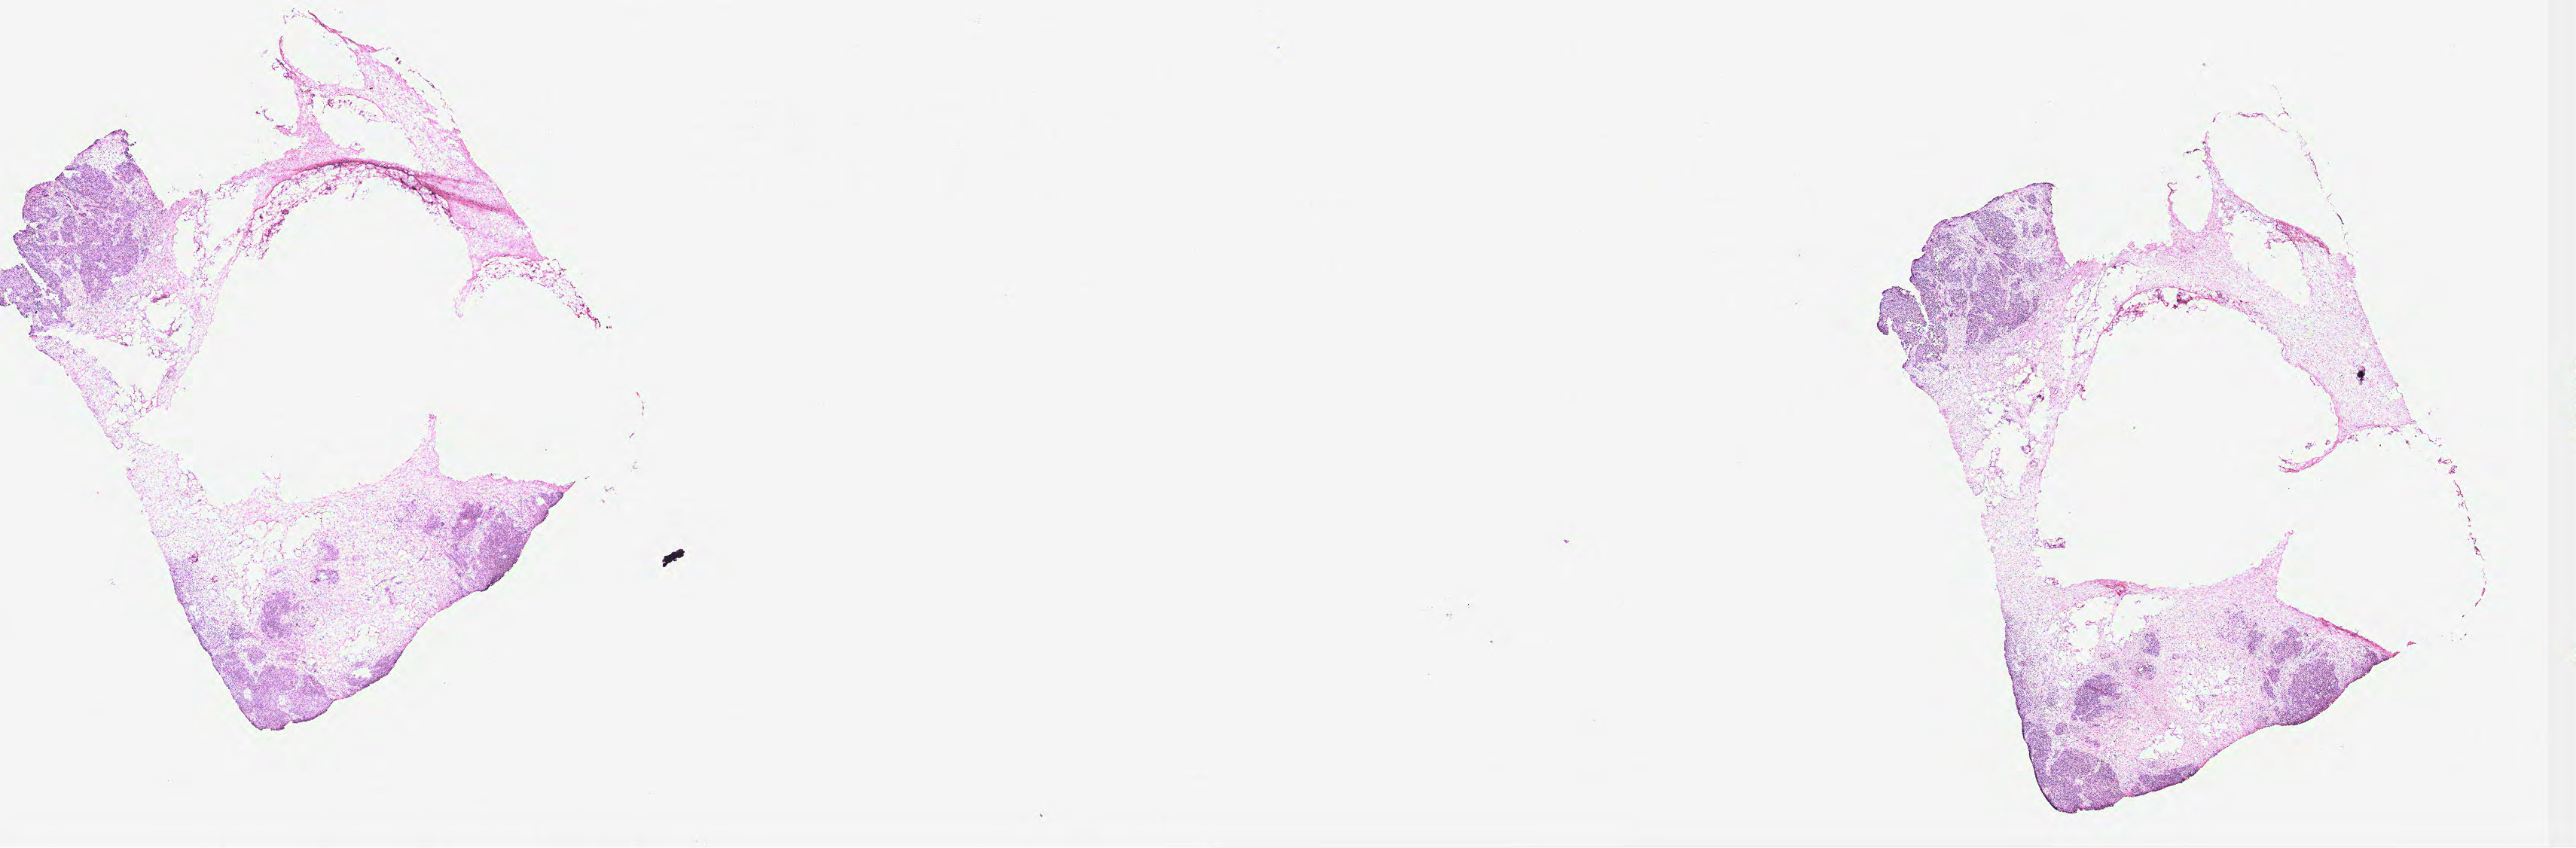
Hematoxylin and eosin (H&E) stained whole-slide image, whole scanned area (about 27.4 x 9.0 mm) shown as a low-resolution overview, ovary, tissue type not recorded. Female patient.
- patient diagnosis: Serous adenocarcinoma, NOS (peritoneum, NOS)